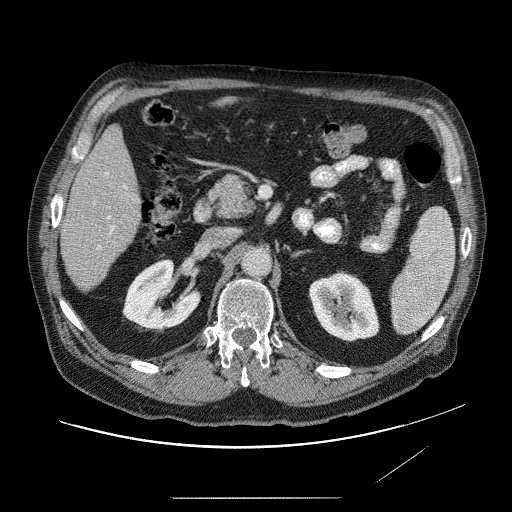
Contrast-enhanced abdominal CT (liver protocol), one axial slice; slice 26 of 89 in the series (ordered by position); reconstruction kernel STANDARD; 120 kVp; soft-tissue window (W 400 / L 40 HU); 2.5 mm slice thickness; 512 × 512 image matrix, field of view 420 × 420 mm. Case-level facts recorded for this patient, not image findings: diagnosis: hepatocellular carcinoma (patient treated with transarterial chemoembolisation; whether this scan precedes or follows treatment is not stated here); TNM stage (as recorded): Stage-IVA; Child-Pugh class: A; tumour differentiation: moderately differentiated; tumour nodularity: multinodular.
Annotated regions visible in this slice (semi-automatic segmentation, software-assisted and operator-edited):
- liver parenchyma outside the tumour (the mass and vessels are separate outlines, so this box may not span the whole liver): bounding box (x1, y1, x2, y2) in pixels: (60, 124, 148, 294)
- liver vessels: (87, 185, 132, 255)